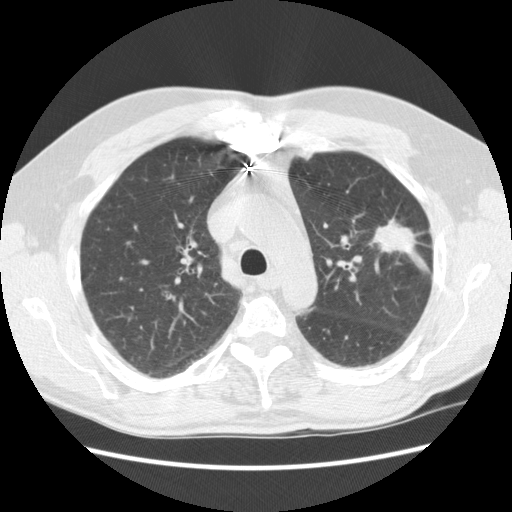
Low-dose screening chest CT, axial slice, baseline screening round, lung window (W 1500 / L -600 HU), 2.5 mm slice thickness, standard (soft-tissue) reconstruction kernel (STANDARD), 512 × 512 image matrix. Male, age 72 years at enrolment. Former smoker at enrolment.
Lesion marked by an expert reader, box from (x=355, y=206) to (x=428, y=260) px. The exam's reader record, not a measurement of the box and not confirmed to be the same lesion: non-calcified nodule or mass ≥4 mm, left upper lobe, 25 × 18 mm, spiculated (stellate) margins, soft tissue attenuation. Official screen result: positive, change unspecified: nodule(s) >= 4 mm or enlarging nodule(s), mass(es), or other non-specific abnormalities suspicious for lung cancer. Lung cancer was diagnosed 35 days after this screen: adenocarcinoma, NOS, left upper lobe, well differentiated (G1), stage IIIB (AJCC 6th edition), 25 mm at pathology.